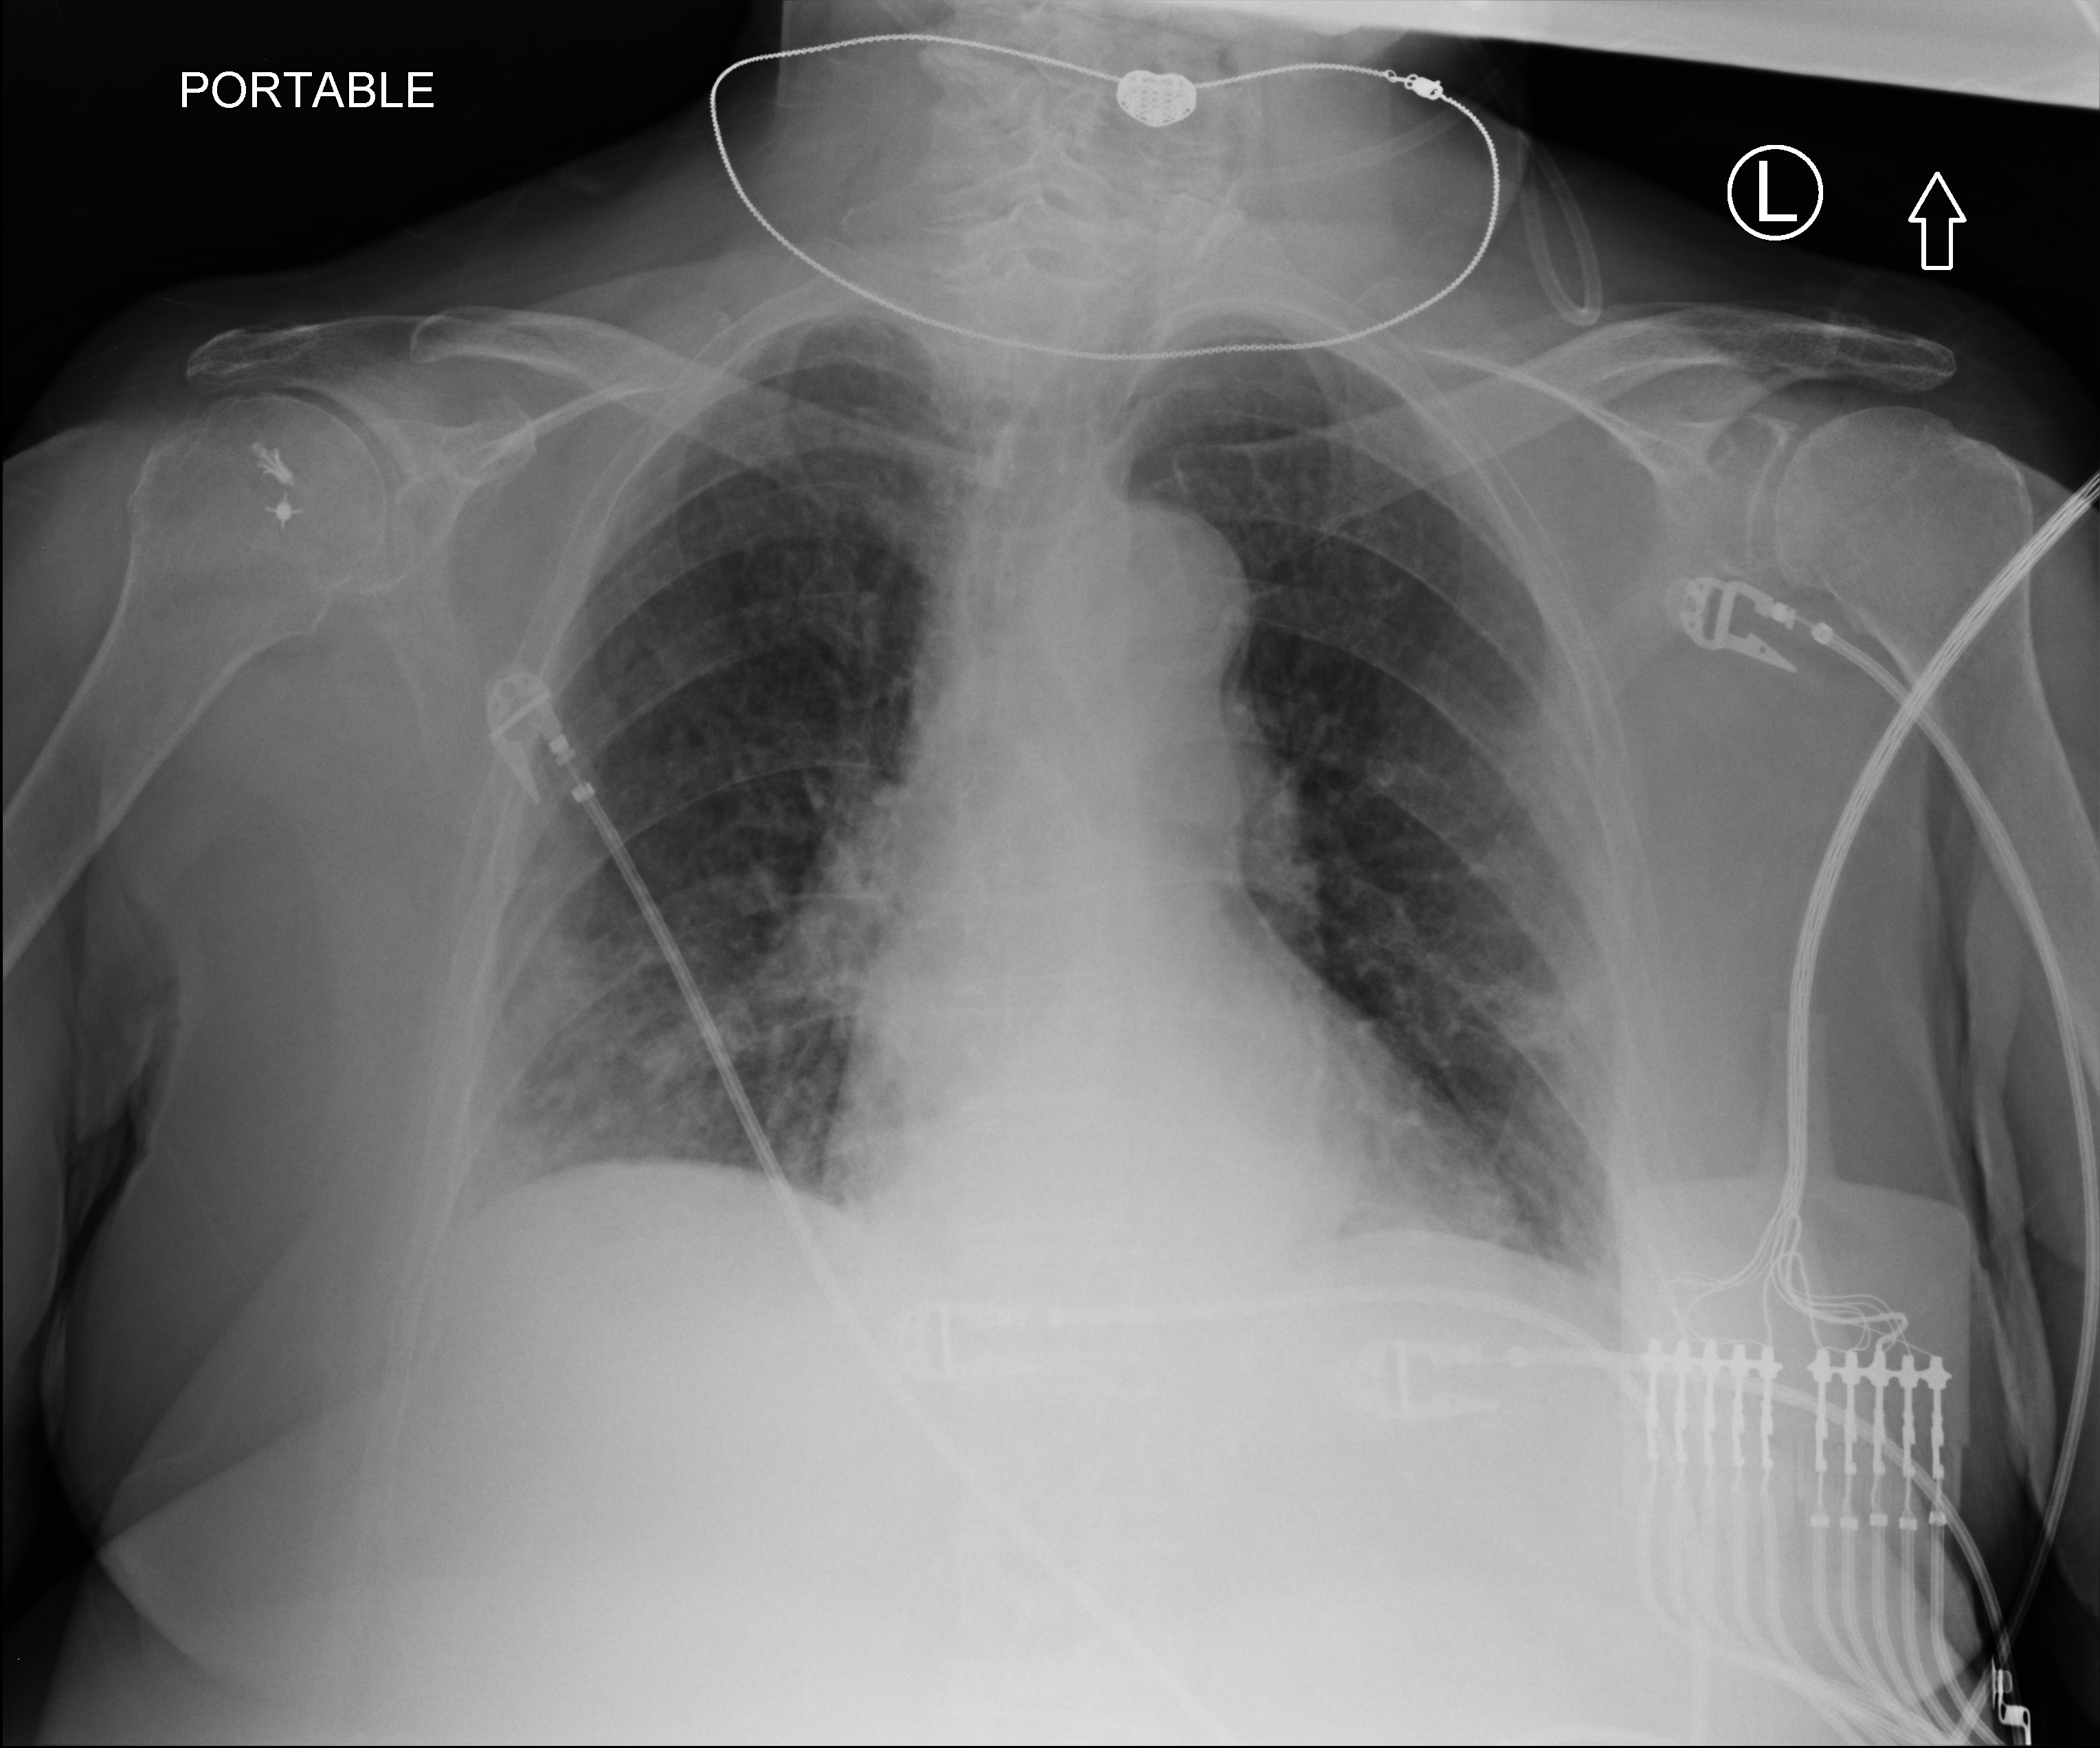
Bedside chest radiograph (computed radiography), anteroposterior (AP) projection. Patient hospitalised with COVID-19; female, aged 75–90 years.
From the hospital-stay record, not from the radiograph (when in the stay this image was taken is not recorded):
- admitted to intensive care during this hospital stay: yes
- mechanically ventilated during this hospital stay: no
- hypertension (admission record): yes